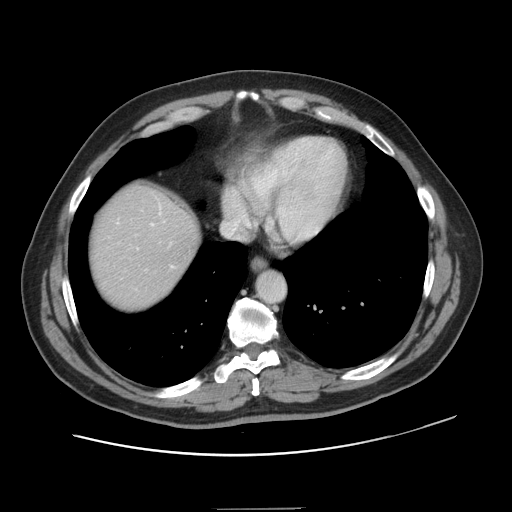
Contrast-enhanced abdominal CT, one axial slice. Slice 133 of 143 in the series (ordered by position). Intravenous contrast given. Soft-tissue window (W 400 / L 40 HU). 512 × 512 image matrix, field of view 402 × 402 mm. Male patient, age 62 years. Case-level facts recorded for this patient, not image findings: diagnosis: colorectal cancer liver metastases, imaged before liver resection; multiple liver metastases: yes; largest metastasis: 2.7 cm; disease in both lobes: no.
Outlined on this slice (manually delineated by an expert):
- hepatic veins: bounding box [x1, y1, x2, y2] px = [118, 213, 172, 267]
- liver: [90, 188, 196, 311]
- planned liver remnant (the part of the liver to remain after resection): [90, 188, 196, 301]